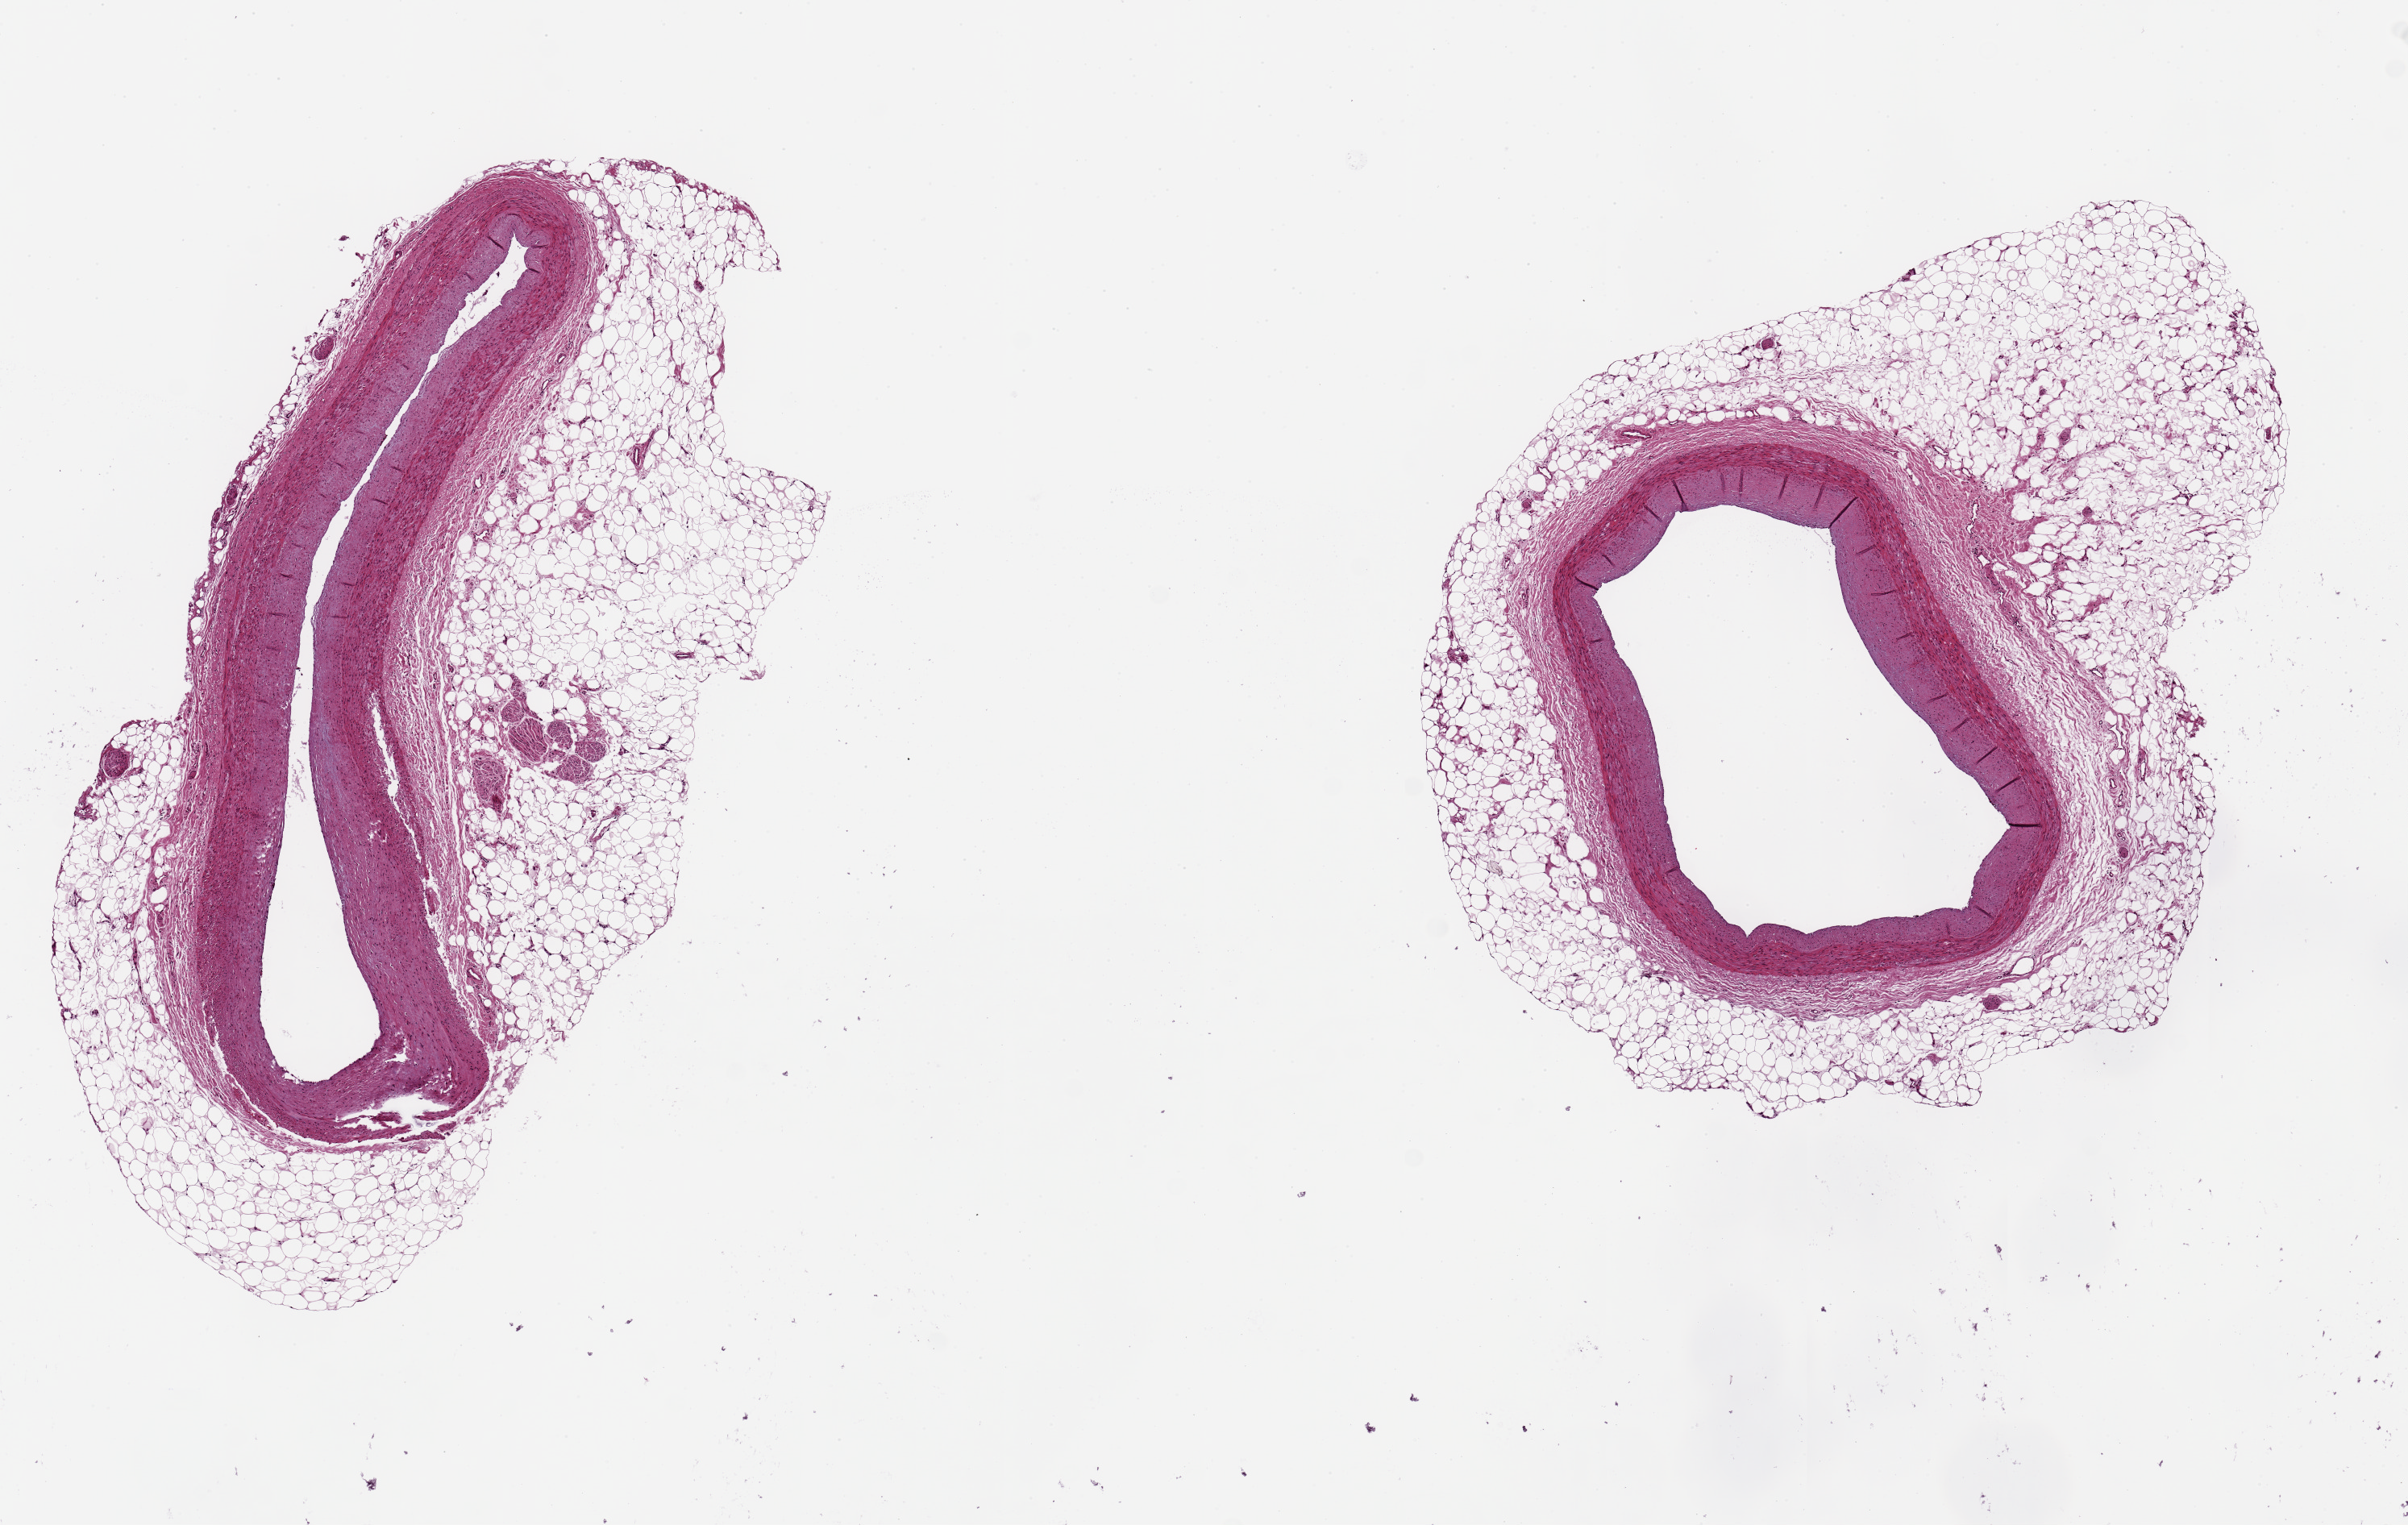
Whole-slide image, haematoxylin and eosin stain, brightfield, low-resolution overview of the scanned area, about 11.8 x 7.5 mm, PAXgene-fixed, paraffin-embedded tissue, sampled site (target tissue): coronary artery, donor tissue sample. Donor sex: male.
• reviewer comment on this tissue sample: 2 aliquots, 3x2mm & 5x1mm, each with ~1mm rim of surrounding fat; minimal occlusive atherosclerosis